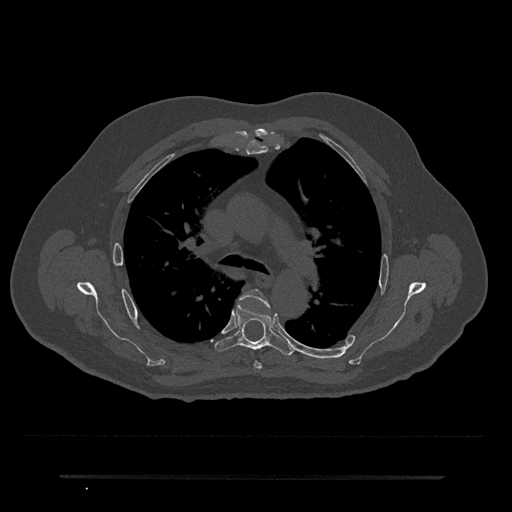
CT including the spine, one axial slice. Position 494 of 797 along the scan axis. 120 kVp. Bone window (W 1800 / L 400 HU). 0.5 mm slice thickness. 512 × 512 image matrix, field of view 437 × 437 mm. Patient: male, 69 years. From the clinical record (not read from this slice): primary cancer: prostate.
Annotated regions visible in this slice (semi-automatically segmented with operator editing):
- T4 vertebra: bounding box [x1, y1, x2, y2] px = [241, 289, 269, 370]
- T5 vertebra: [215, 301, 295, 355]